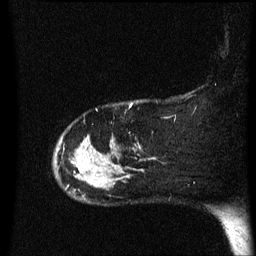
Breast MRI (dynamic contrast-enhanced), one sagittal slice; slice 55 of 60 in the series (ordered by position); dynamic contrast-enhanced series, image 2 of 3 at this slice position (ordered by acquisition); 1.5 T; TE 4.2 ms, TR 8.4 ms; 2.2 mm slice thickness; 256 × 256 image matrix. Patient: female, 47 years.
Annotated regions visible in this slice (semi-automatic segmentation, software-assisted and operator-edited):
- analysis volume of interest (the breast-tissue region the enhancement analysis was run in; not a lesion): bounding box <54,136,141,201> (left, top, right, bottom; pixels)
- tumour enhancement mask (voxels above the 70 % enhancement threshold inside the analysis volume of interest): <78,150,107,184>